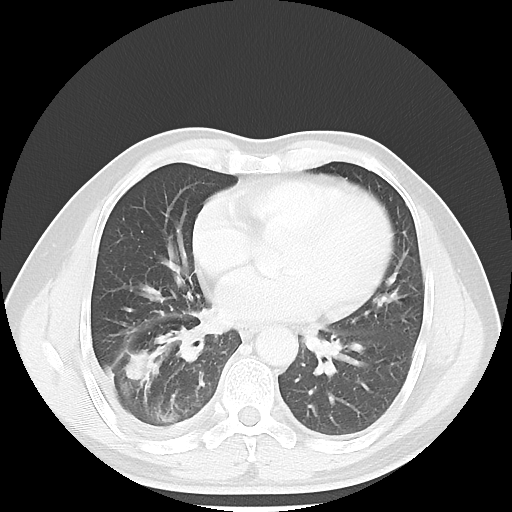
Chest CT, one axial slice; position 24 of 56 along the scan axis; reconstruction kernel LUNG; 120 kVp; lung window (W 1500 / L -600 HU); 5 mm slice thickness; 512 × 512 image matrix. Male patient, age 56 years. From the clinical record (not read from this slice): clinical TNM (as recorded): T2 N3 M1.
Annotated regions visible in this slice (rectangle marked by the reading radiologist):
- lung tumour (recorded histology: adenocarcinoma): bounding box <119,345,163,384> (left, top, right, bottom; pixels)